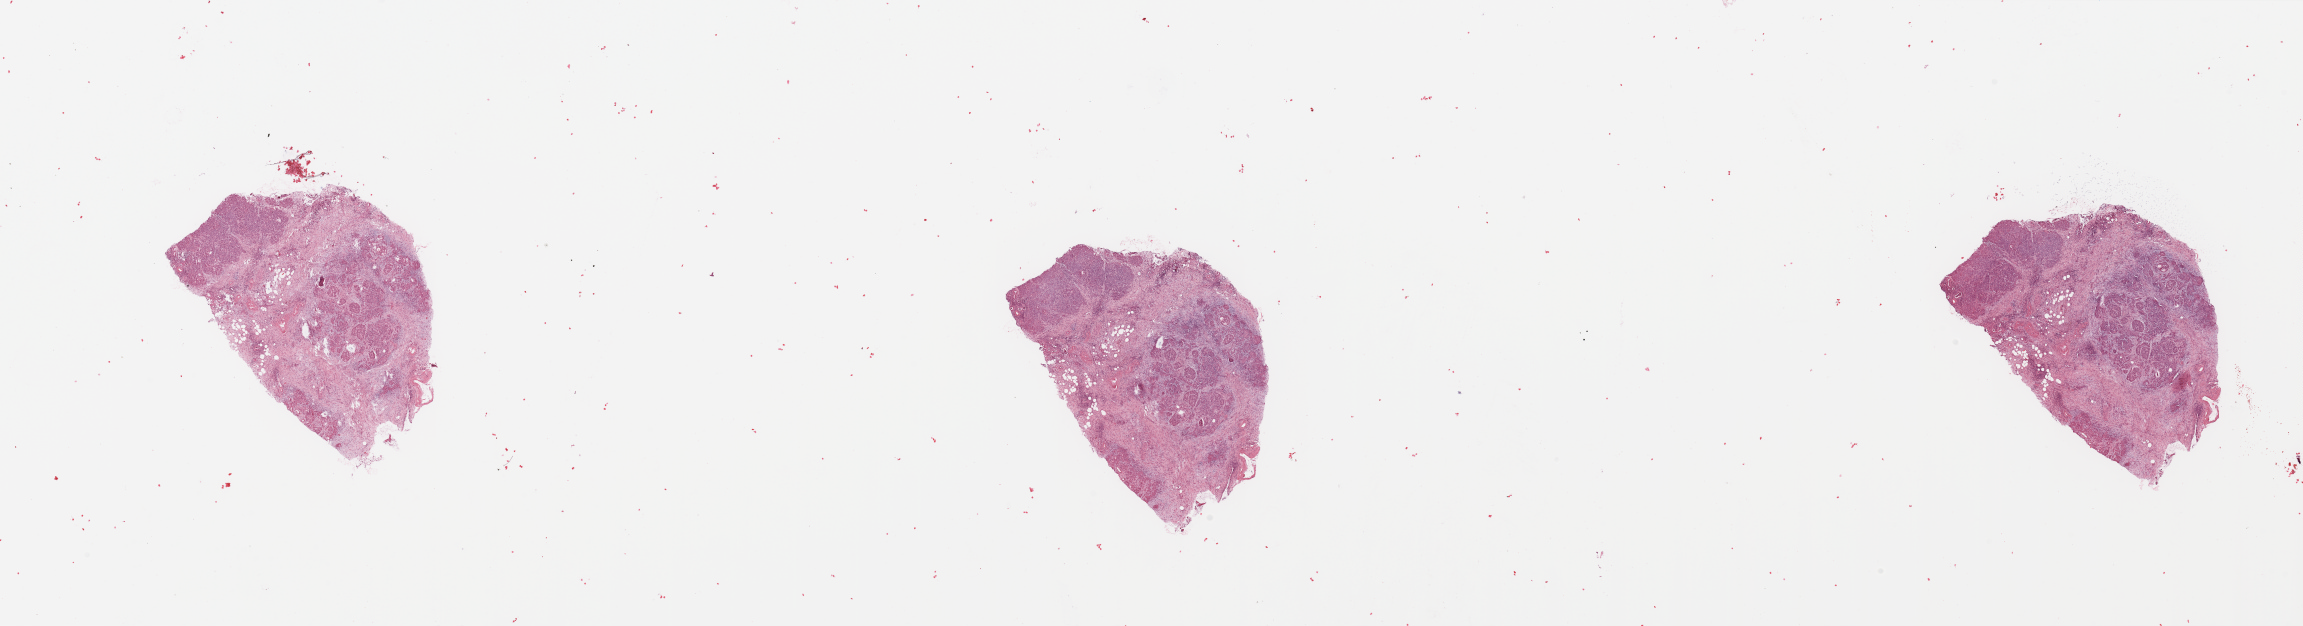
H&E-stained whole-slide image, low-resolution overview of the scanned area, about 36.4 x 9.9 mm, normal (non-tumour) tissue sample, pancreas. Patient: male, age 73 years.
This section: normal (non-tumour) tissue from the same patient. Patient diagnosis: Infiltrating duct carcinoma, NOS.